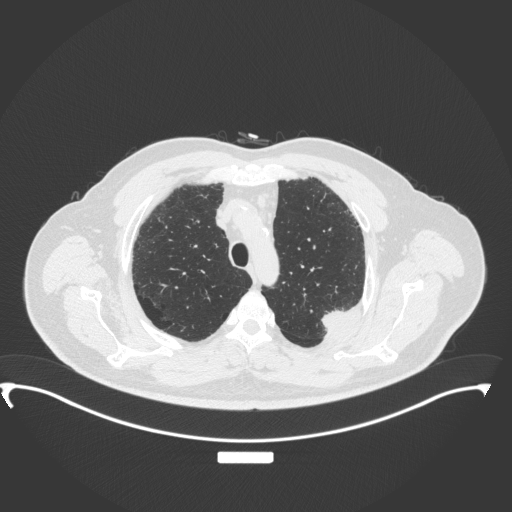
Chest CT, one axial slice. Slice 285 of 350 in the series (ordered by position). Reconstruction kernel B31f. Lung window (W 1500 / L -600 HU). 1 mm slice thickness. 512 × 512 image matrix, field of view 459 × 459 mm. Patient: male, 64 years. Case-level facts recorded for this patient, not image findings: clinical TNM (as recorded): T1c N1 M1.
Structures marked on this image (bounding box drawn by a radiologist):
- lung tumour (recorded histology: adenocarcinoma): bounding box <316,304,356,333> (left, top, right, bottom; pixels)